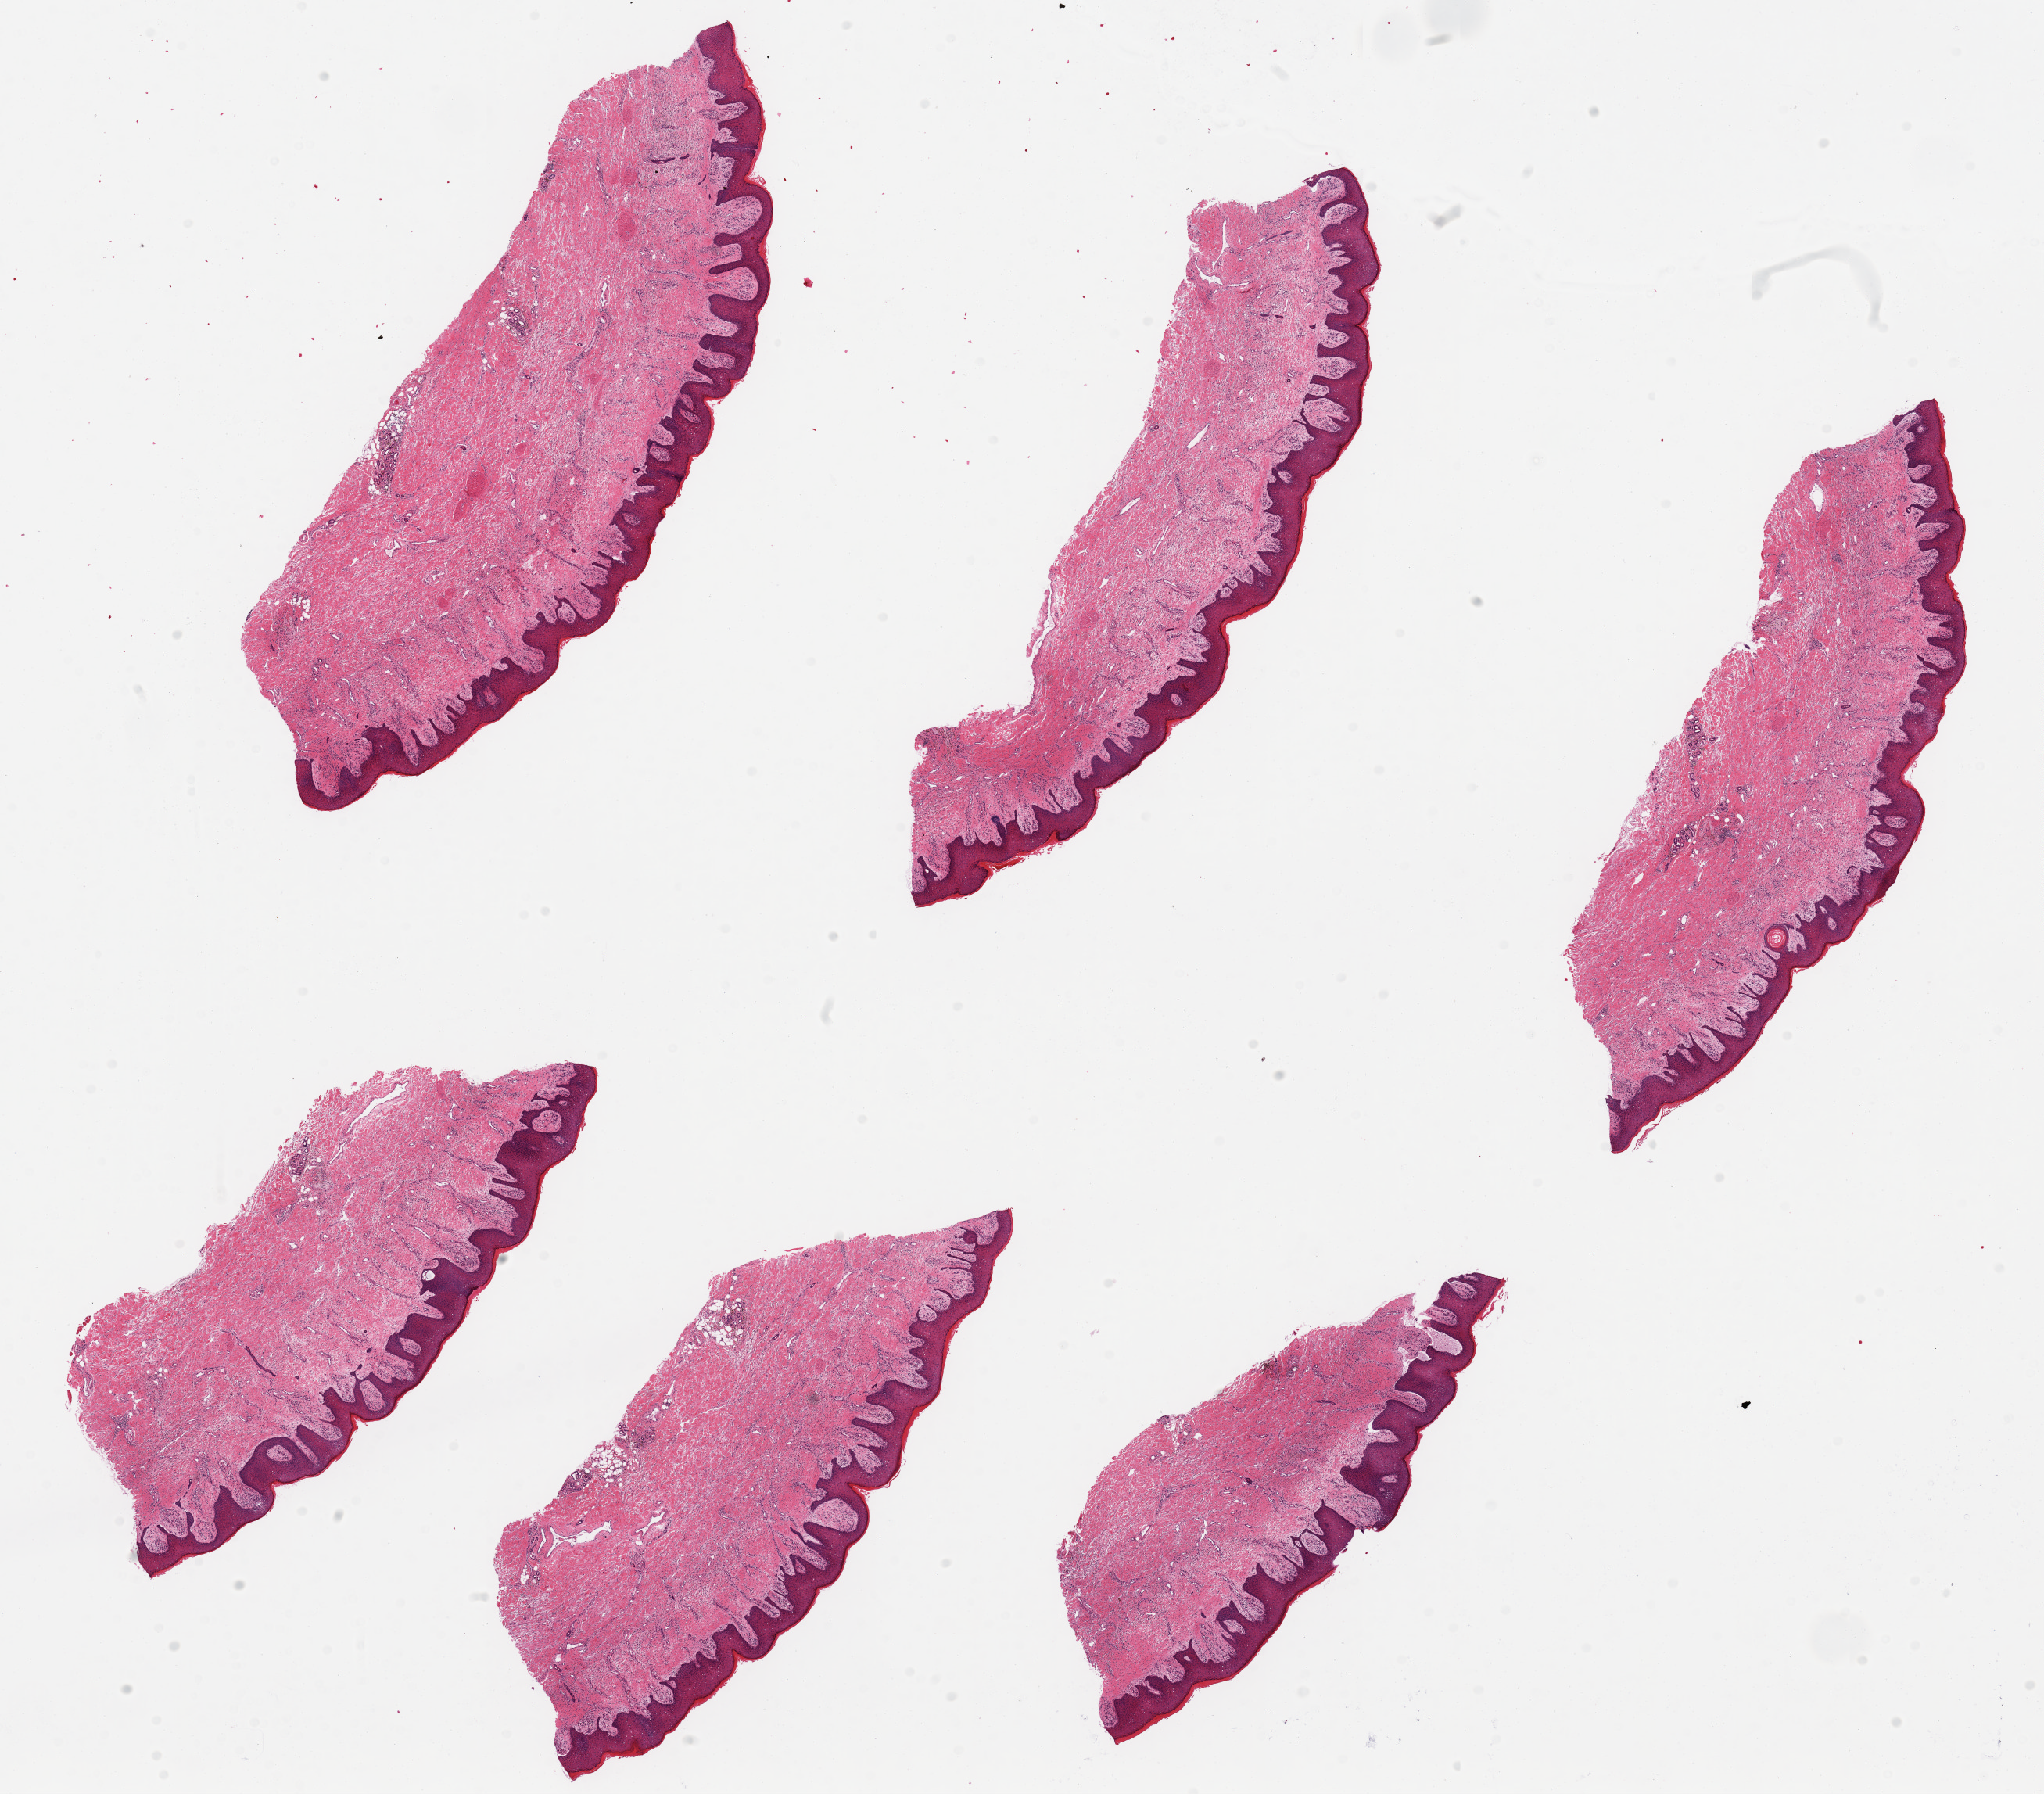
Hematoxylin and eosin (H&E) whole-slide image — a low-resolution overview of the entire scanned area, about 20.7 x 18.1 mm. PAXgene-fixed paraffin-embedded (PFPE) section. Sampled site (target tissue): skin of lower leg. Donor tissue sample. Male donor.
Reviewer comment on this tissue sample: 6 pieces; psoriasiform epidermal hyperplasia; epidermis over 200 microns thick; stasis dermatitis and dermal fibrosis and vascular accentuation with scar/keloid like features; possible dermal mucin (sample from the right leg).